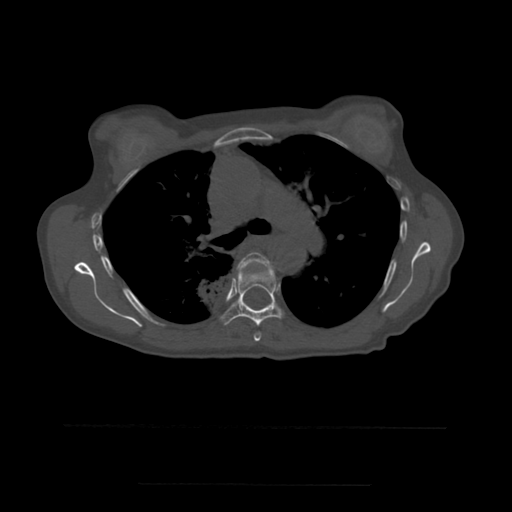
CT including the spine, one axial slice; position 379 of 544 along the scan axis; bone window (W 1800 / L 400 HU); 1.25 mm slice thickness; 512 × 512 image matrix, field of view 350 × 350 mm. Patient age 58 years. Case-level facts recorded for this patient, not image findings: primary cancer: lung.
Outlined on this slice (semi-automatically segmented with operator editing):
- T5 vertebra: bounding box <238,253,273,342> (left, top, right, bottom; pixels)
- T6 vertebra: <220,265,286,326>